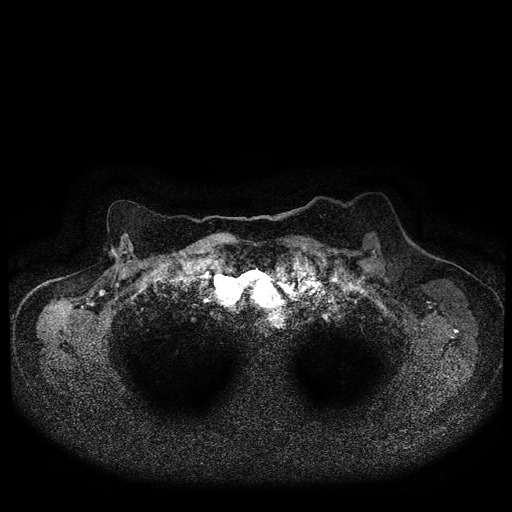
Breast MRI (dynamic contrast-enhanced, multi-phase), one axial slice; slice 77 of 116 in the series (ordered by position); dynamic contrast-enhanced series, time point 2 of 5 at this slice position (early post-contrast); 1.5 T; TE 2.7 ms, TR 5.4 ms; 2 mm slice thickness; 512 × 512 image matrix, field of view 340 × 340 mm. Female patient, age 72 years.
Annotated regions visible in this slice (semi-automatically segmented with operator editing):
- breast lesion (labelled 'tumour' in the annotation; benign lesions carry a separate 'benign' label): bounding box <110,249,118,258> (left, top, right, bottom; pixels)